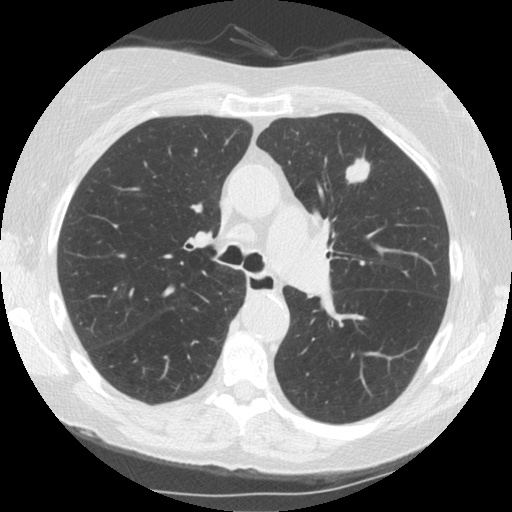
Low-dose screening chest CT, one axial slice. Position 95 of 153 along the scan axis. Reconstruction kernel STANDARD. 120 kVp. Lung window (W 1500 / L -600 HU). 2.5 mm slice thickness. 512 × 512 image matrix, field of view 330 × 330 mm.
Outlined on this slice (outlined manually by an expert reader):
- lesion 1 (tumor, upper lobe of left lung): bounding box [x1, y1, x2, y2] px = [346, 158, 370, 183]